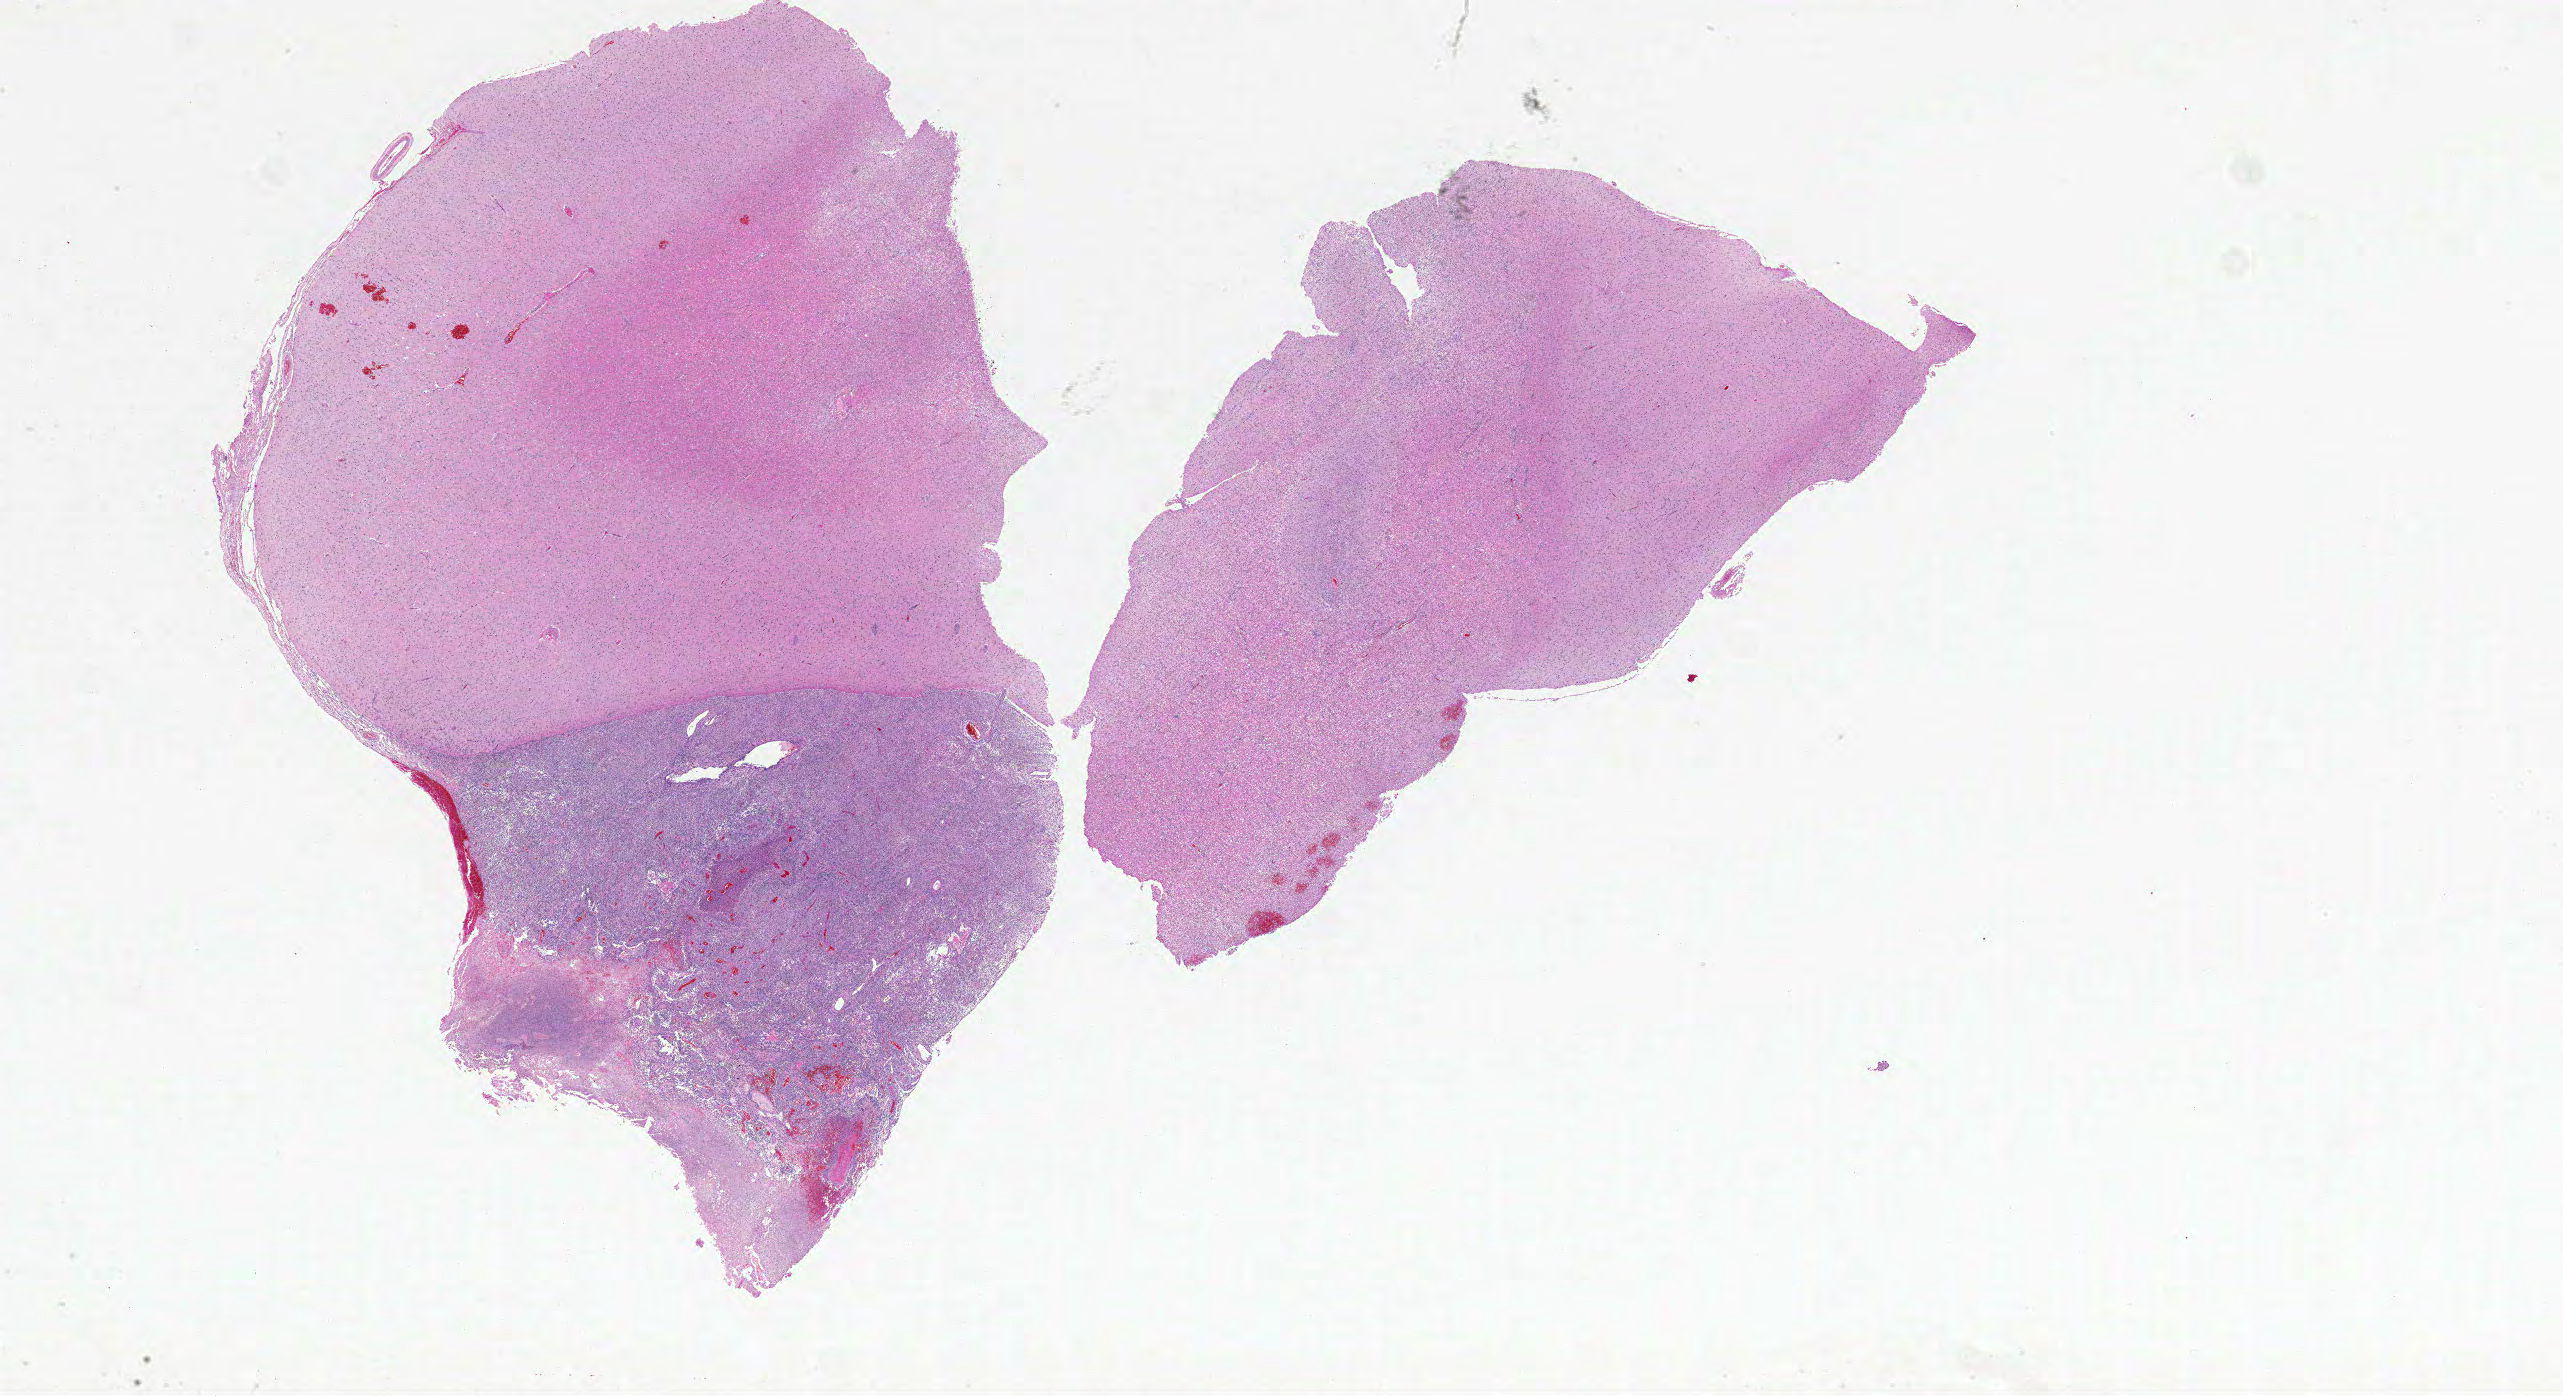
Digitized H&E tissue section (whole slide), shown as a low-resolution overview of the whole scanned area (about 41.0 x 22.3 mm, acquisition: 20x scan). Formalin-fixed paraffin-embedded (FFPE) diagnostic section. Brain, primary tumour sample. Female patient; age at initial diagnosis 65 years.
Histologic diagnosis: Glioblastoma.